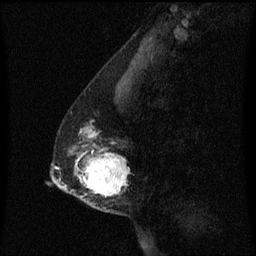
Breast MRI (dynamic contrast-enhanced), one sagittal slice; dynamic contrast-enhanced series, image 2 of 3 at this slice position (ordered by acquisition); 1.5 T; TE 4.2 ms, TR 8.4 ms; 2 mm slice thickness; 256 × 256 image matrix, field of view 200 × 200 mm. Female patient, age 40 years. From the clinical record (not read from this slice): setting: breast cancer imaged before/during neoadjuvant chemotherapy; receptor status: triple-negative.
Outlined on this slice (semi-automatic segmentation, software-assisted and operator-edited):
- analysis volume of interest (the breast-tissue region the enhancement analysis was run in; not a lesion): bounding box <60,128,131,215> (left, top, right, bottom; pixels)
- tumour enhancement mask (voxels above the 70 % enhancement threshold inside the analysis volume of interest): <80,130,129,197>